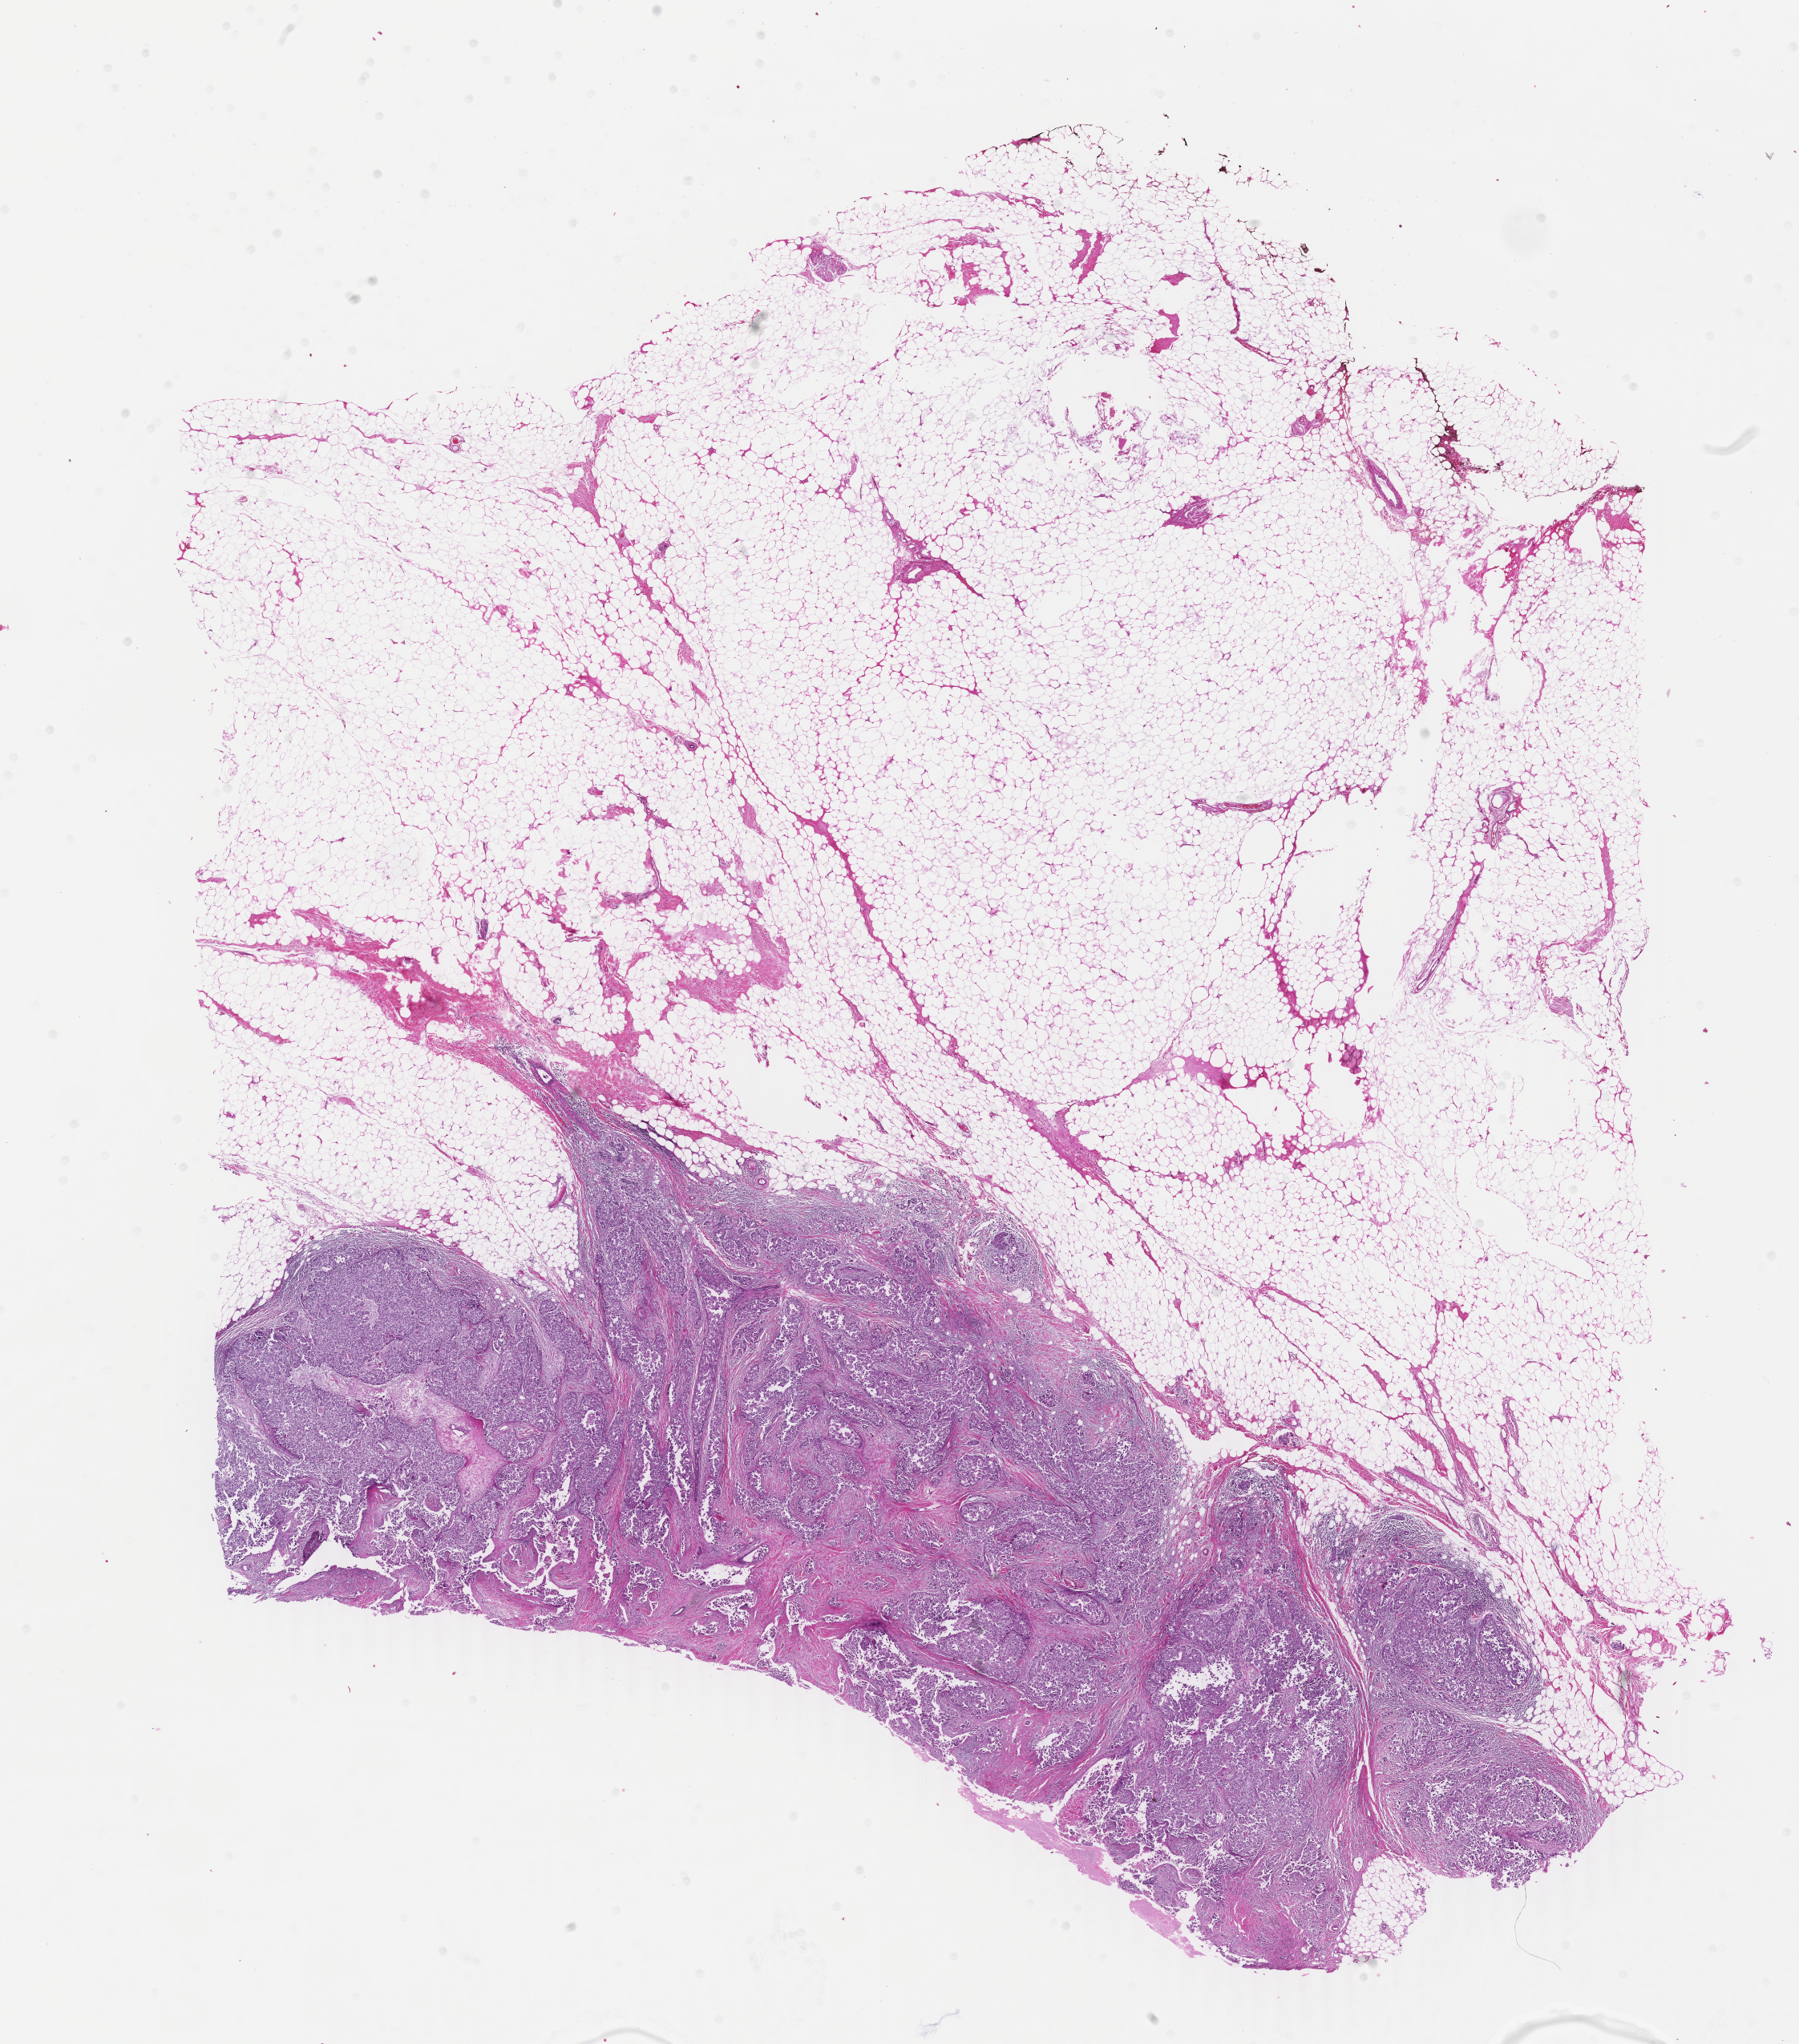
Hematoxylin and eosin (H&E) stained whole-slide image, a low-resolution overview of the entire scanned area, about 17.8 x 20.3 mm (slide scanned at 40x); FFPE section; primary tumour sample from the breast. Patient: female, age at initial diagnosis 52 years.
• TNM: T2 N0 (i-) M0
• histologic diagnosis: Infiltrating duct carcinoma, NOS
• AJCC pathologic stage: IIA (6th edition)
• laterality: left
• lymph nodes positive (case pathology): 0 of 2 examined